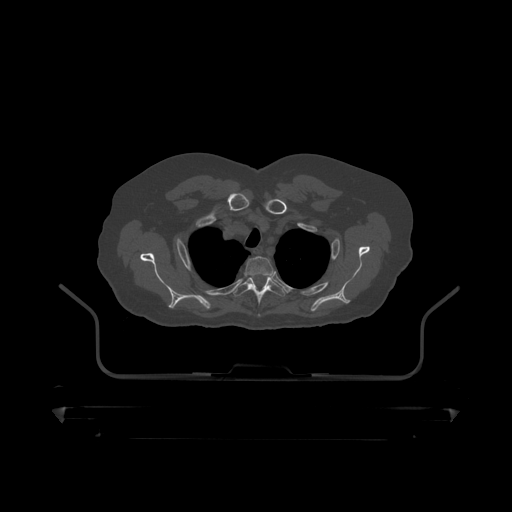
CT including the spine, one axial slice. Slice 365 of 390 in the series (ordered by position). Bone window (W 1800 / L 400 HU). 1.25 mm slice thickness. 512 × 512 image matrix, field of view 650 × 650 mm. Patient: male, 60 years. Case-level facts recorded for this patient, not image findings: primary cancer: prostate.
Outlined on this slice (semi-automatic segmentation, software-assisted and operator-edited):
- T2 vertebra: bounding box [x1, y1, x2, y2] px = [245, 257, 275, 277]
- T3 vertebra: [234, 276, 285, 318]